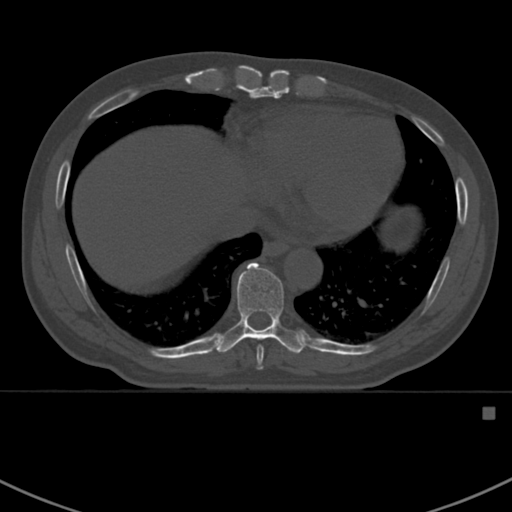
CT including the spine, one axial slice. Position 386 of 412 along the scan axis. Reconstruction kernel Br40s. Bone window (W 1800 / L 400 HU). 1.5 mm slice thickness. 512 × 512 image matrix, field of view 358 × 358 mm. Patient: male, 59 years. From the clinical record (not read from this slice): primary cancer: prostate.
Outlined on this slice (semi-automatic segmentation, software-assisted and operator-edited):
- T8 vertebra: bounding box [x1, y1, x2, y2] px = [256, 346, 264, 370]
- T9 vertebra: [215, 262, 306, 354]